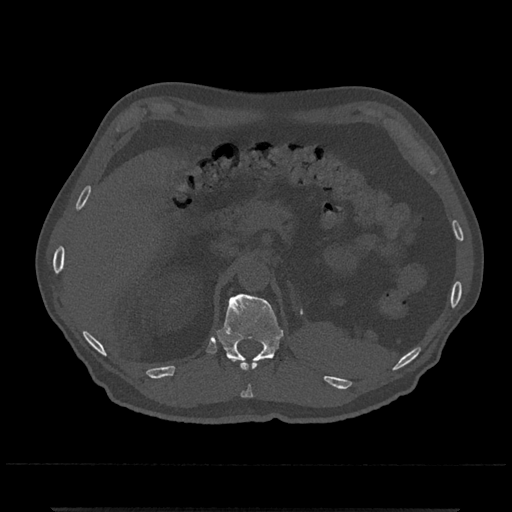
CT including the spine, one axial slice; position 447 of 797 along the scan axis; reconstruction kernel Br40s/3; bone window (W 1800 / L 400 HU); 0.5 mm slice thickness; 512 × 512 image matrix, field of view 393 × 393 mm. Patient: male, 67 years. Case-level facts recorded for this patient, not image findings: primary cancer: prostate.
Structures marked on this image (semi-automatically segmented with operator editing):
- T11 vertebra: box from (x=229, y=358) to (x=257, y=398) px
- T12 vertebra: (x=216, y=293)–(x=284, y=366)